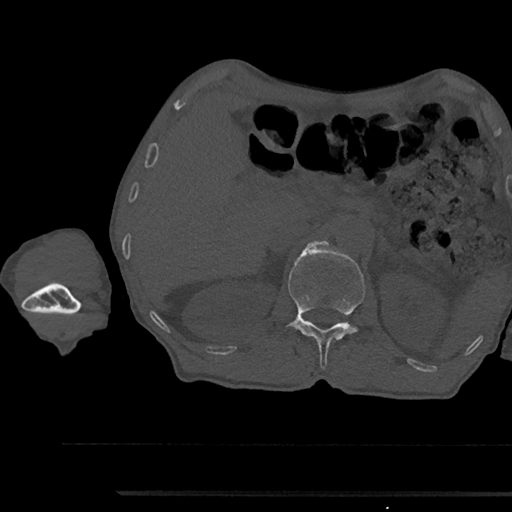
CT including the spine, one axial slice; slice 635 of 797 in the series (ordered by position); reconstruction kernel Br40s/3; 120 kVp; bone window (W 1800 / L 400 HU); 512 × 512 image matrix. Patient: male, 79 years. Case-level facts recorded for this patient, not image findings: primary cancer: prostate.
Annotated regions visible in this slice (semi-automatic segmentation, software-assisted and operator-edited):
- L1 vertebra: bounding box [x1, y1, x2, y2] px = [288, 242, 365, 369]